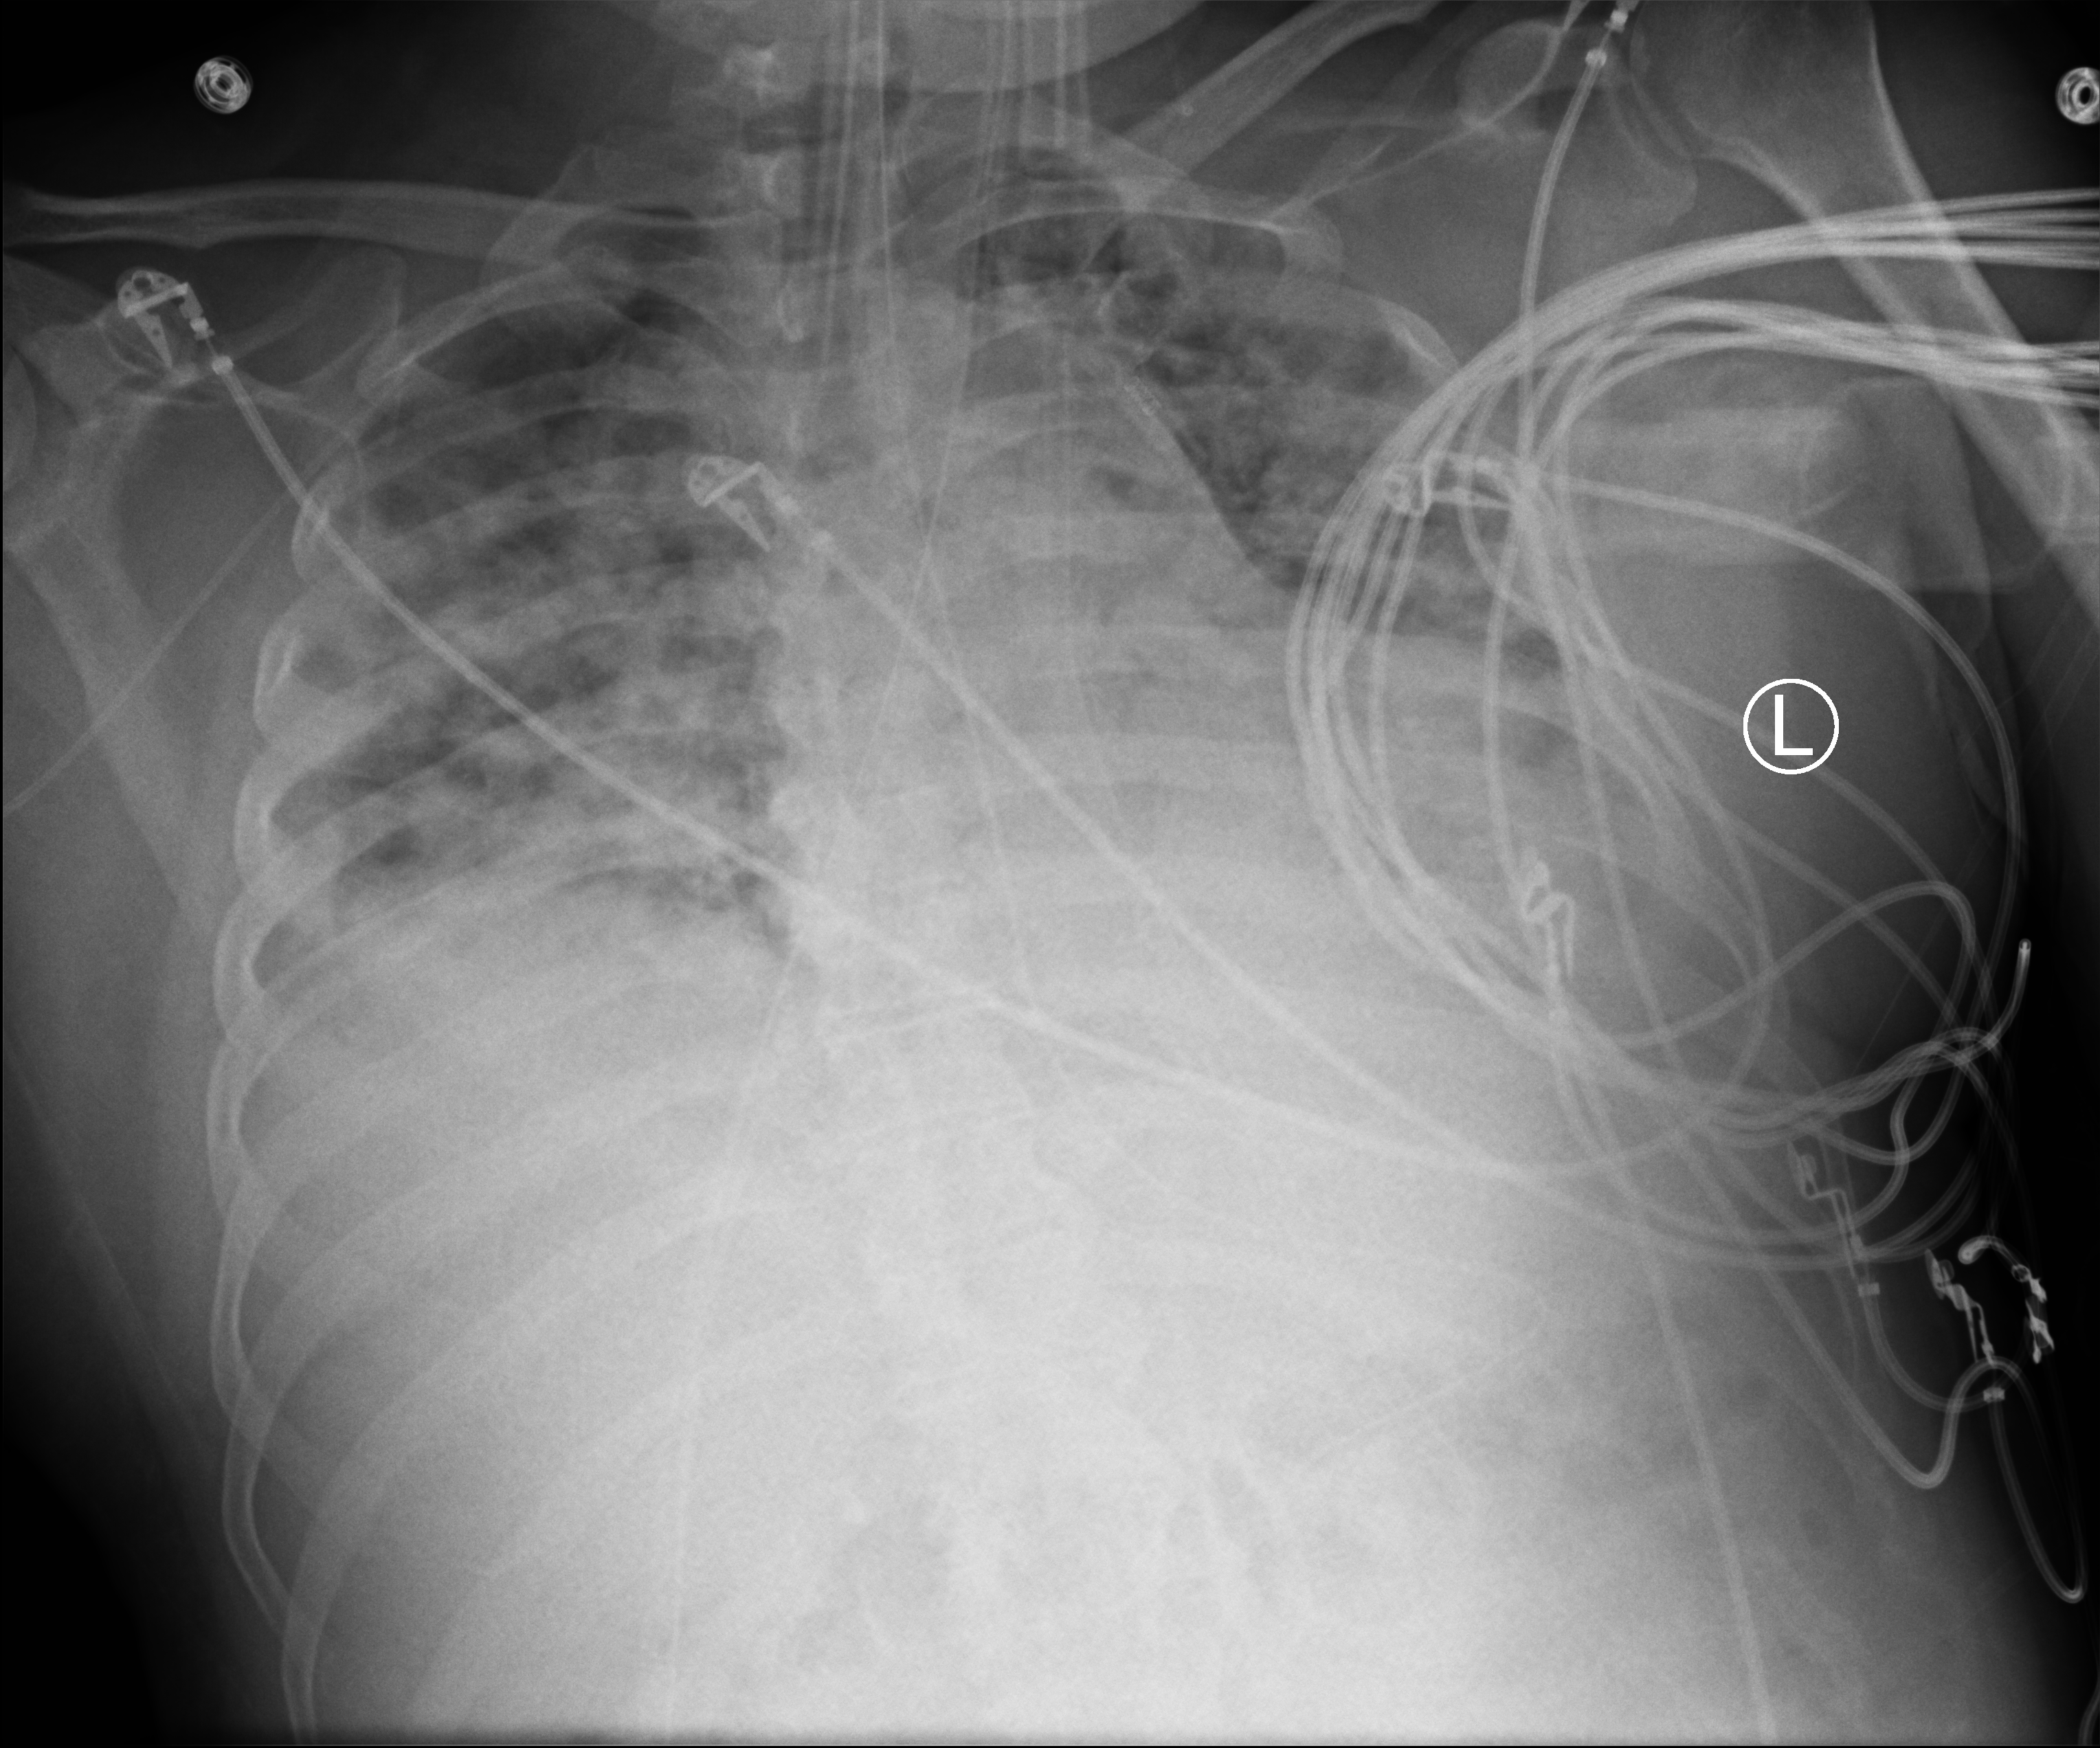
Portable chest radiograph. Male patient hospitalised with COVID-19, age 18–59 years.
From the hospital-stay record, not from the radiograph (when in the stay this image was taken is not recorded):
- length of hospital stay: 26 days
- mechanically ventilated during this hospital stay: yes
- admitted to intensive care during this hospital stay: yes